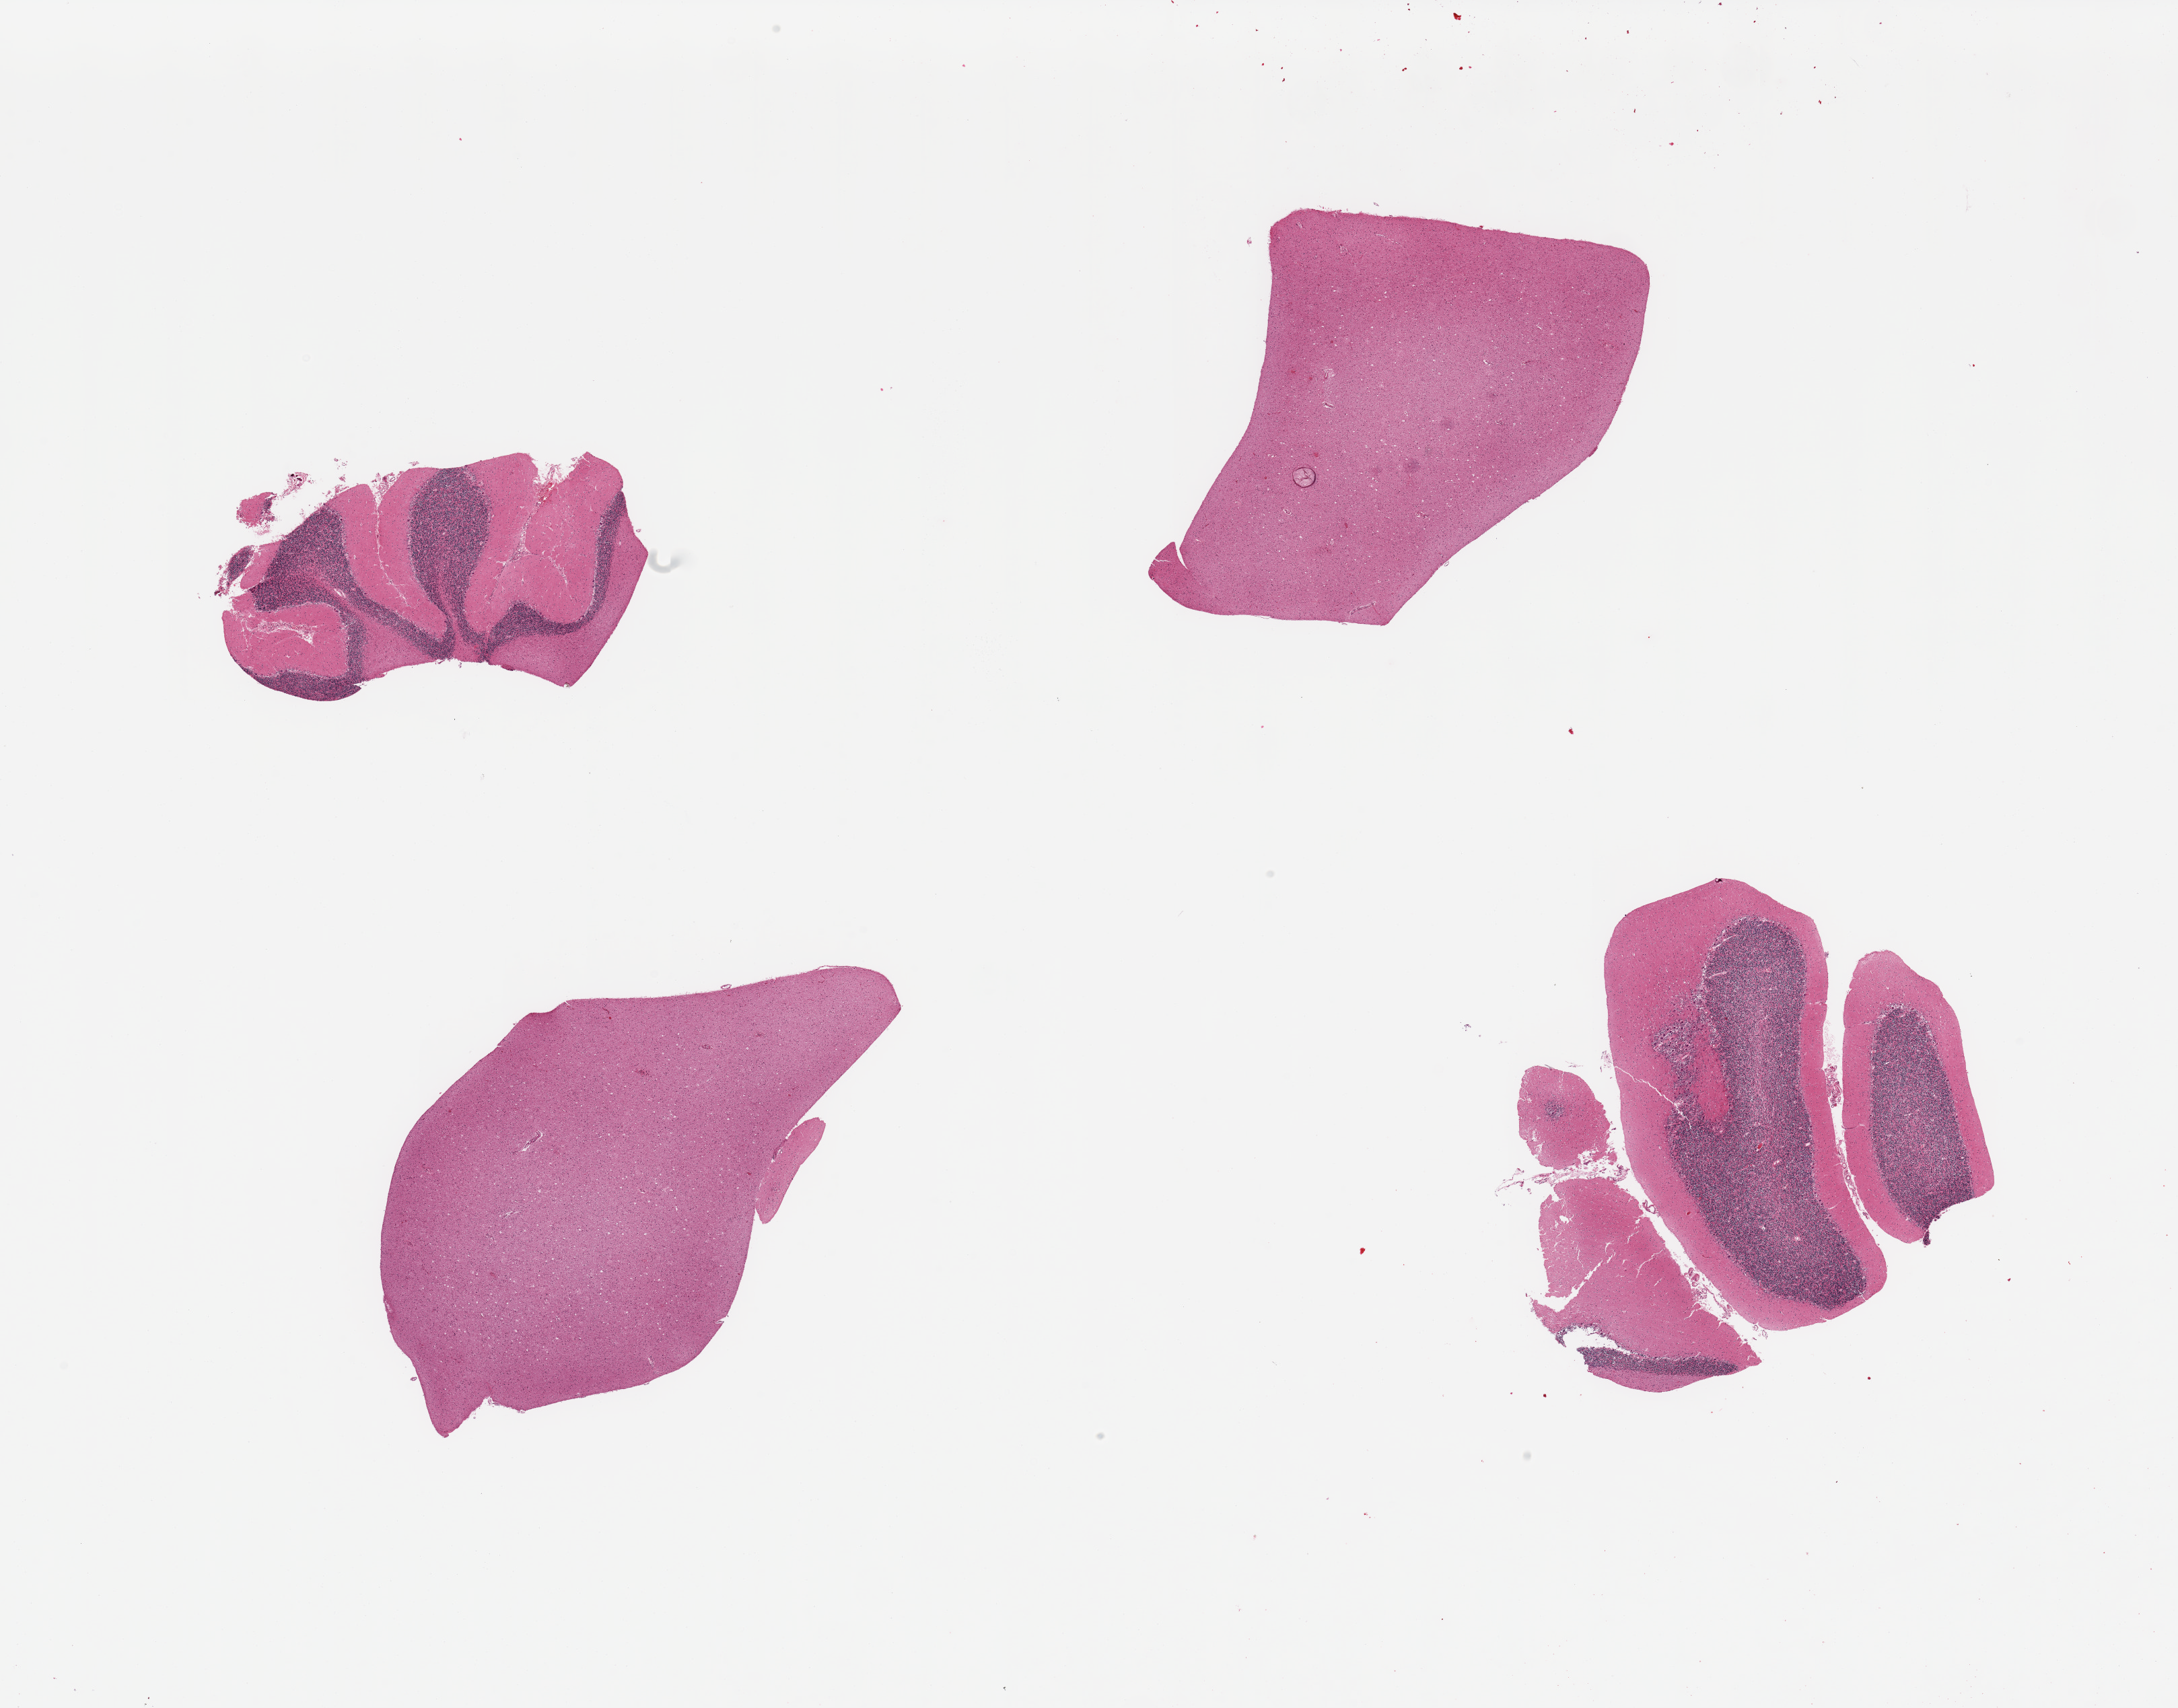
Whole-slide image, H&E stain, brightfield — shown as a low-resolution overview of the whole scanned area (about 25.6 x 20.1 mm), PAXgene-fixed paraffin-embedded (PFPE) section, section of cerebellum (target tissue), donor tissue sample. Donor sex: male.
Reviewer comment on this tissue sample: 4 pieces; 2 are cerebellum; 2 resemble cortex.